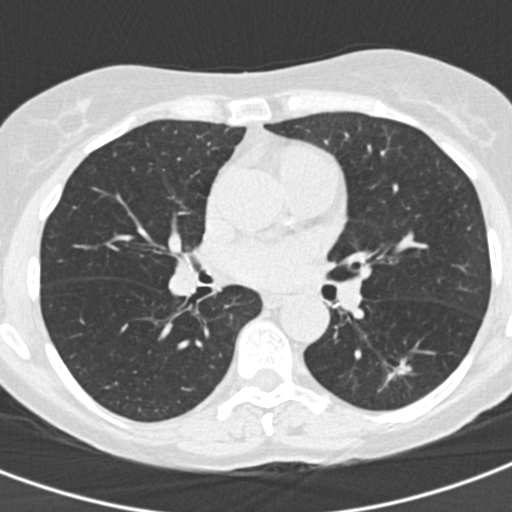
Low-dose screening chest CT, one axial slice. Position 83 of 155 along the scan axis. Lung window (W 1500 / L -600 HU). 2 mm slice thickness. 512 × 512 image matrix, field of view 282 × 282 mm.
Outlined on this slice (manually delineated by an expert):
- lesion 1 (tumor, lower lobe of left lung): bounding box [x1, y1, x2, y2] px = [378, 359, 413, 392]